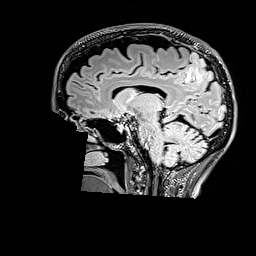
Brain MRI from a brain-tumour surgery series, one sagittal slice. T2 FLAIR. 256 × 256 image matrix, field of view 256 × 256 mm. From the clinical record (not read from this slice): histopathology: Astrocytoma; WHO grade: 3; IDH mutation: yes; tumour location: Right Parietal.
Outlined on this slice (outlined manually by an expert reader):
- tumour: bounding box <184,56,213,83> (left, top, right, bottom; pixels)
- tumour: <185,52,214,83>